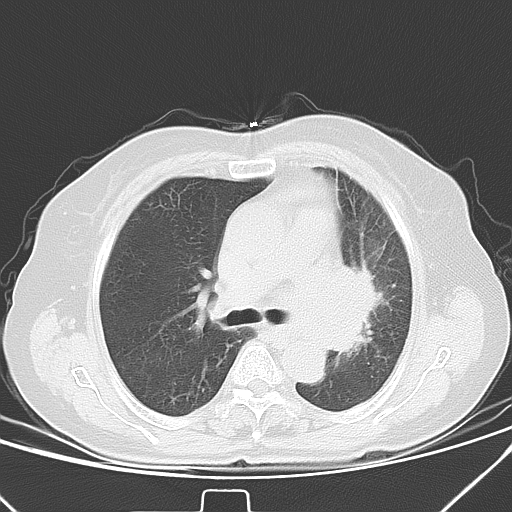
Chest CT, one axial slice; position 25 of 40 along the scan axis; 120 kVp; lung window (W 1500 / L -600 HU); 5 mm slice thickness; 512 × 512 image matrix. Female patient, age 59 years. Case-level facts recorded for this patient, not image findings: clinical TNM (as recorded): T3 N1 M0; histopathological grade: G3.
Outlined on this slice (rectangle marked by the reading radiologist):
- lung tumour (recorded histology: small cell carcinoma): bounding box [x1, y1, x2, y2] px = [336, 256, 384, 360]